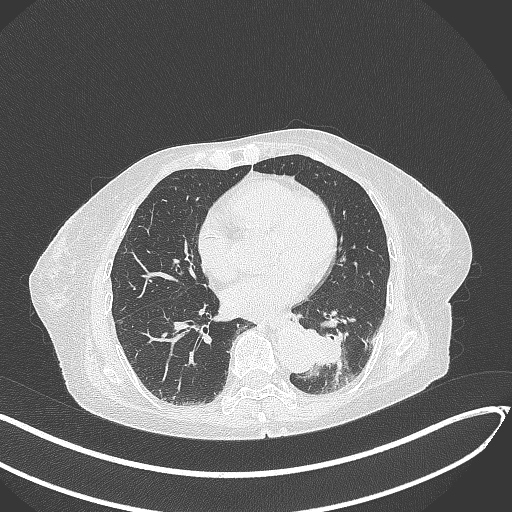
Chest CT, one axial slice; position 100 of 324 along the scan axis; 120 kVp; lung window (W 1500 / L -600 HU); 1 mm slice thickness; 512 × 512 image matrix, field of view 400 × 400 mm. Female patient, age 82 years. Case-level facts recorded for this patient, not image findings: clinical TNM (as recorded): T1b N0 M1.
Outlined on this slice (rectangle marked by the reading radiologist):
- lung tumour (recorded histology: adenocarcinoma): bounding box [x1, y1, x2, y2] px = [300, 329, 352, 378]